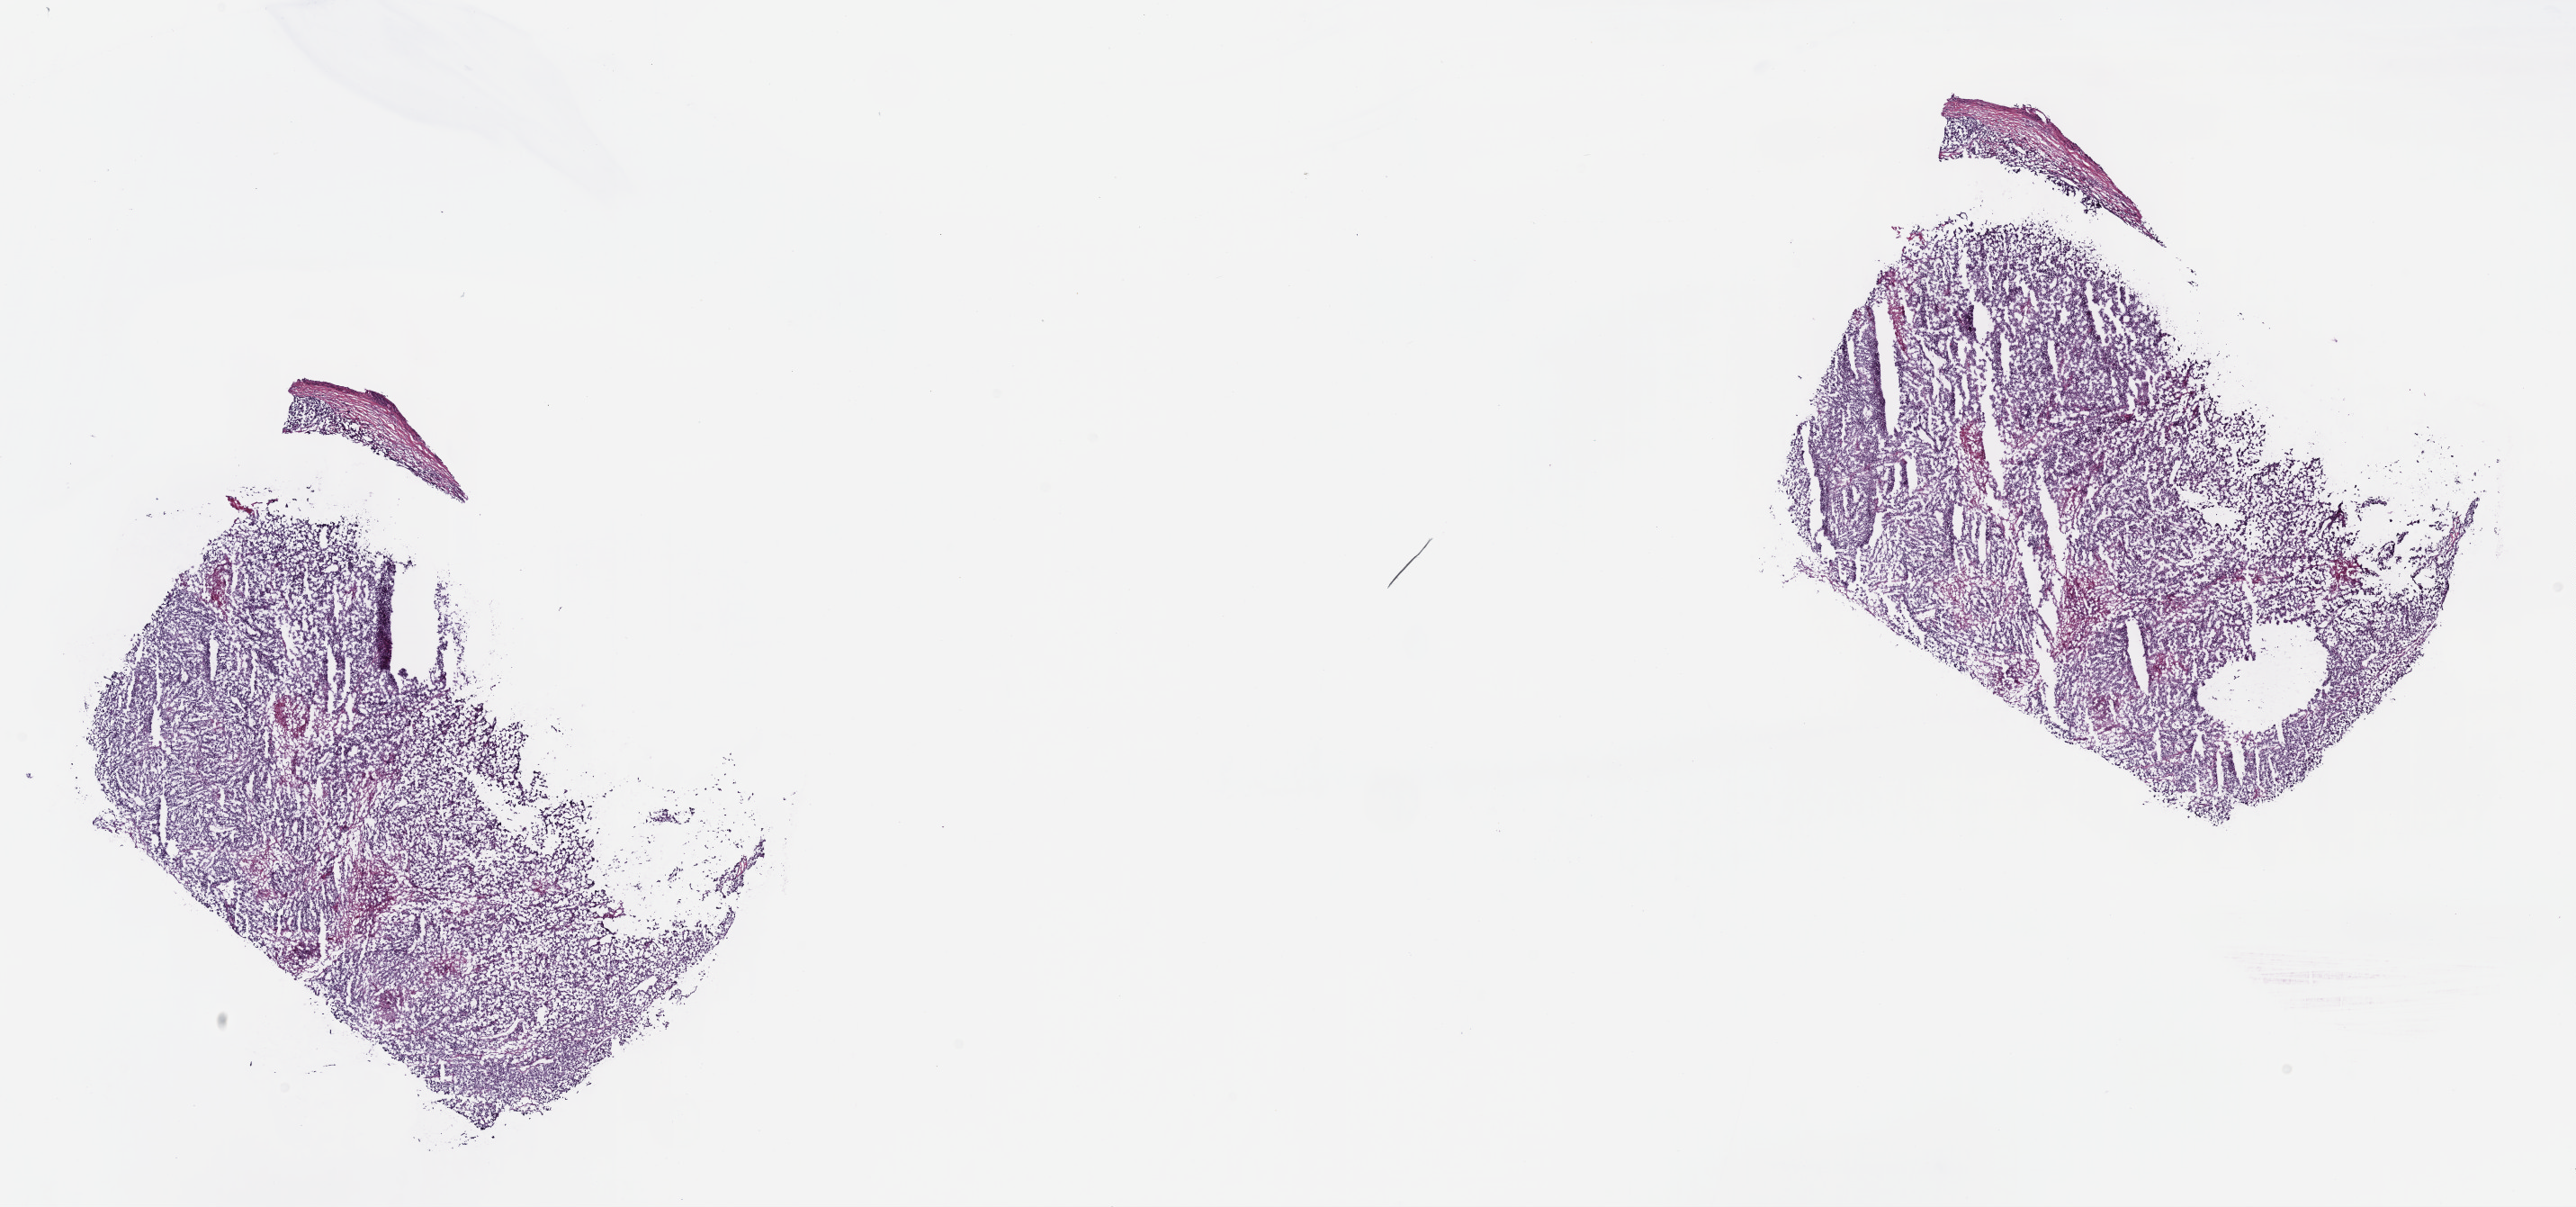
Digitized H&E tissue section (whole slide), shown as a low-resolution overview of the whole scanned area (about 23.2 x 10.8 mm, slide scanned at 40x). Frozen section from the top of the tissue portion. Metastatic tumour sample. Patient: male, age at initial diagnosis 18 years.
This section: metastatic tumour tissue. Patient diagnosis: Malignant melanoma, NOS.